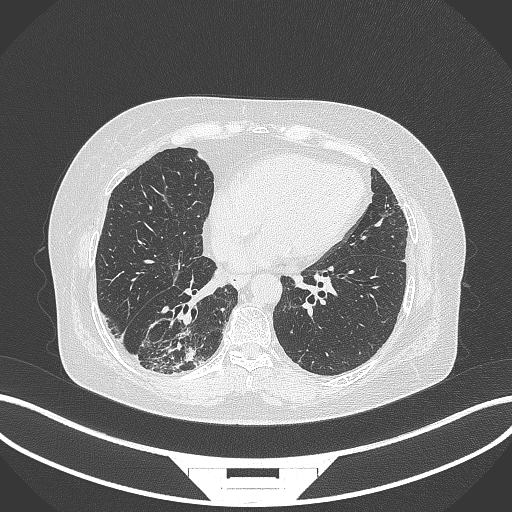
Chest CT, one axial slice. Slice 81 of 296 in the series (ordered by position). Reconstruction kernel B70f. 120 kVp. Lung window (W 1500 / L -600 HU). 1 mm slice thickness. 512 × 512 image matrix, field of view 400 × 400 mm. Female patient, age 65 years. Case-level facts recorded for this patient, not image findings: clinical TNM (as recorded): T2b N1 M0; histopathological grade: G1.
Annotated regions visible in this slice (rectangle marked by the reading radiologist):
- lung tumour (recorded histology: adenocarcinoma): box from (x=136, y=315) to (x=196, y=373) px